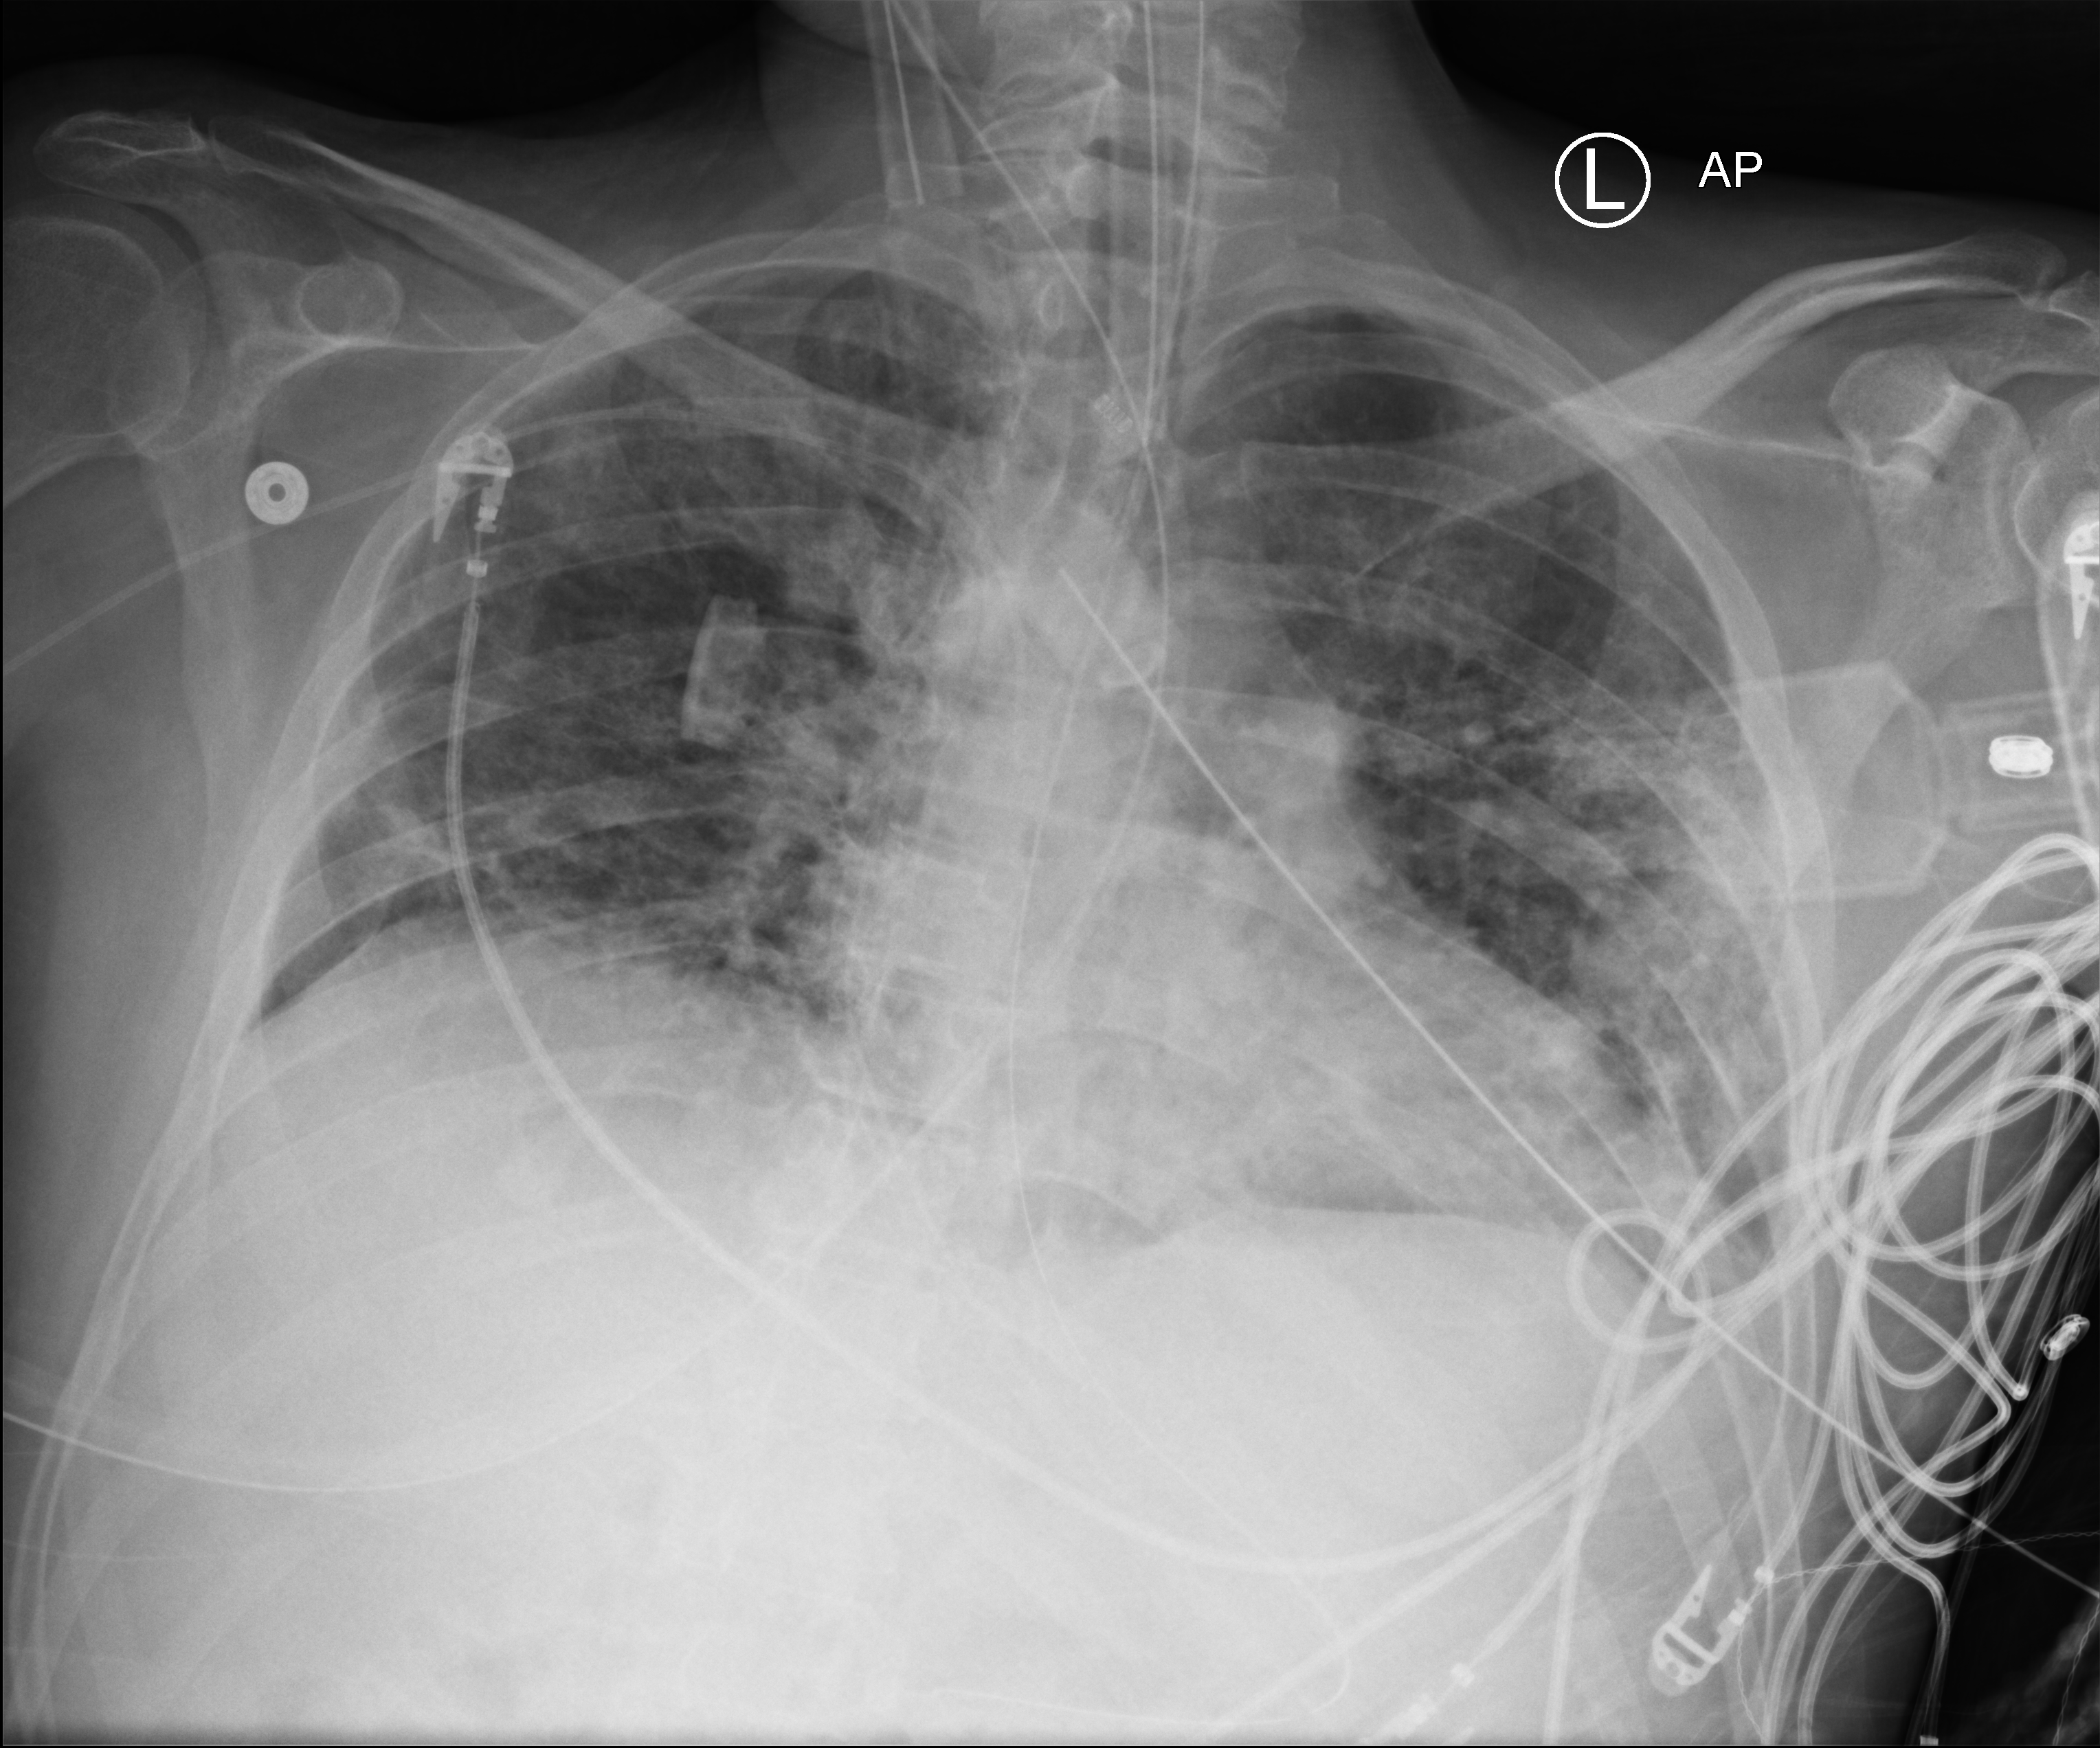
Bedside chest radiograph (computed radiography); anteroposterior (AP) projection. Patient hospitalised with COVID-19; male, aged 18–59 years.
From the hospital-stay record, not from the radiograph (when in the stay this image was taken is not recorded): other chronic lung disease (admission record): no; chronic kidney disease (admission record): no; admitted to intensive care during this hospital stay: yes.